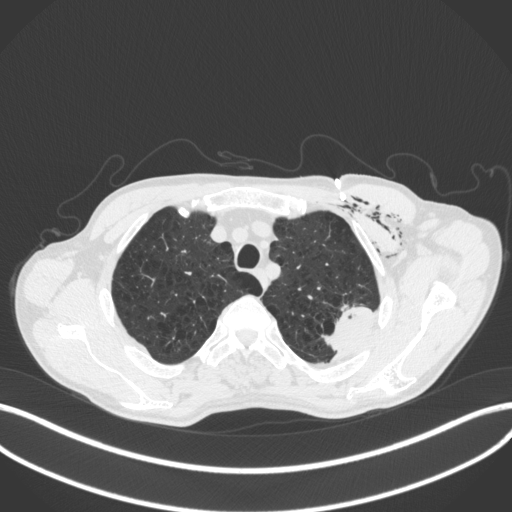
Chest CT, one axial slice. Position 343 of 416 along the scan axis. Reconstruction kernel B31f. 120 kVp. Lung window (W 1500 / L -600 HU). 1 mm slice thickness. 512 × 512 image matrix, field of view 400 × 400 mm. Patient: male, 58 years. From the clinical record (not read from this slice): clinical TNM (as recorded): T3 N0 M0.
Annotated regions visible in this slice (rectangle marked by the reading radiologist):
- lung tumour (recorded histology: adenocarcinoma): bounding box <317,306,376,360> (left, top, right, bottom; pixels)